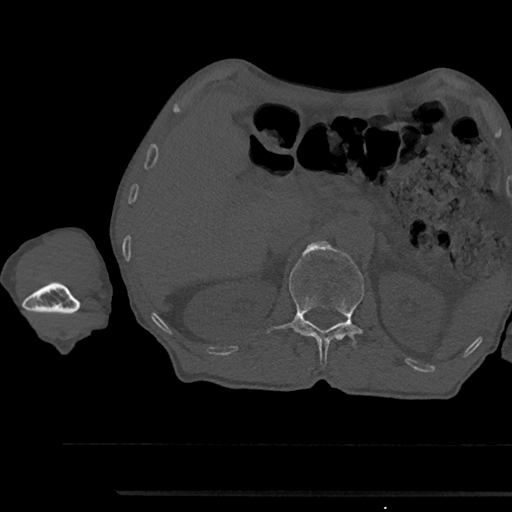
CT including the spine, one axial slice; reconstruction kernel Br40s/3; 120 kVp; bone window (W 1800 / L 400 HU); 0.5 mm slice thickness; 512 × 512 image matrix. Patient: male, 79 years. From the clinical record (not read from this slice): primary cancer: prostate.
Outlined on this slice (semi-automatically segmented with operator editing):
- L1 vertebra: bounding box (x1, y1, x2, y2) in pixels: (282, 241, 364, 363)